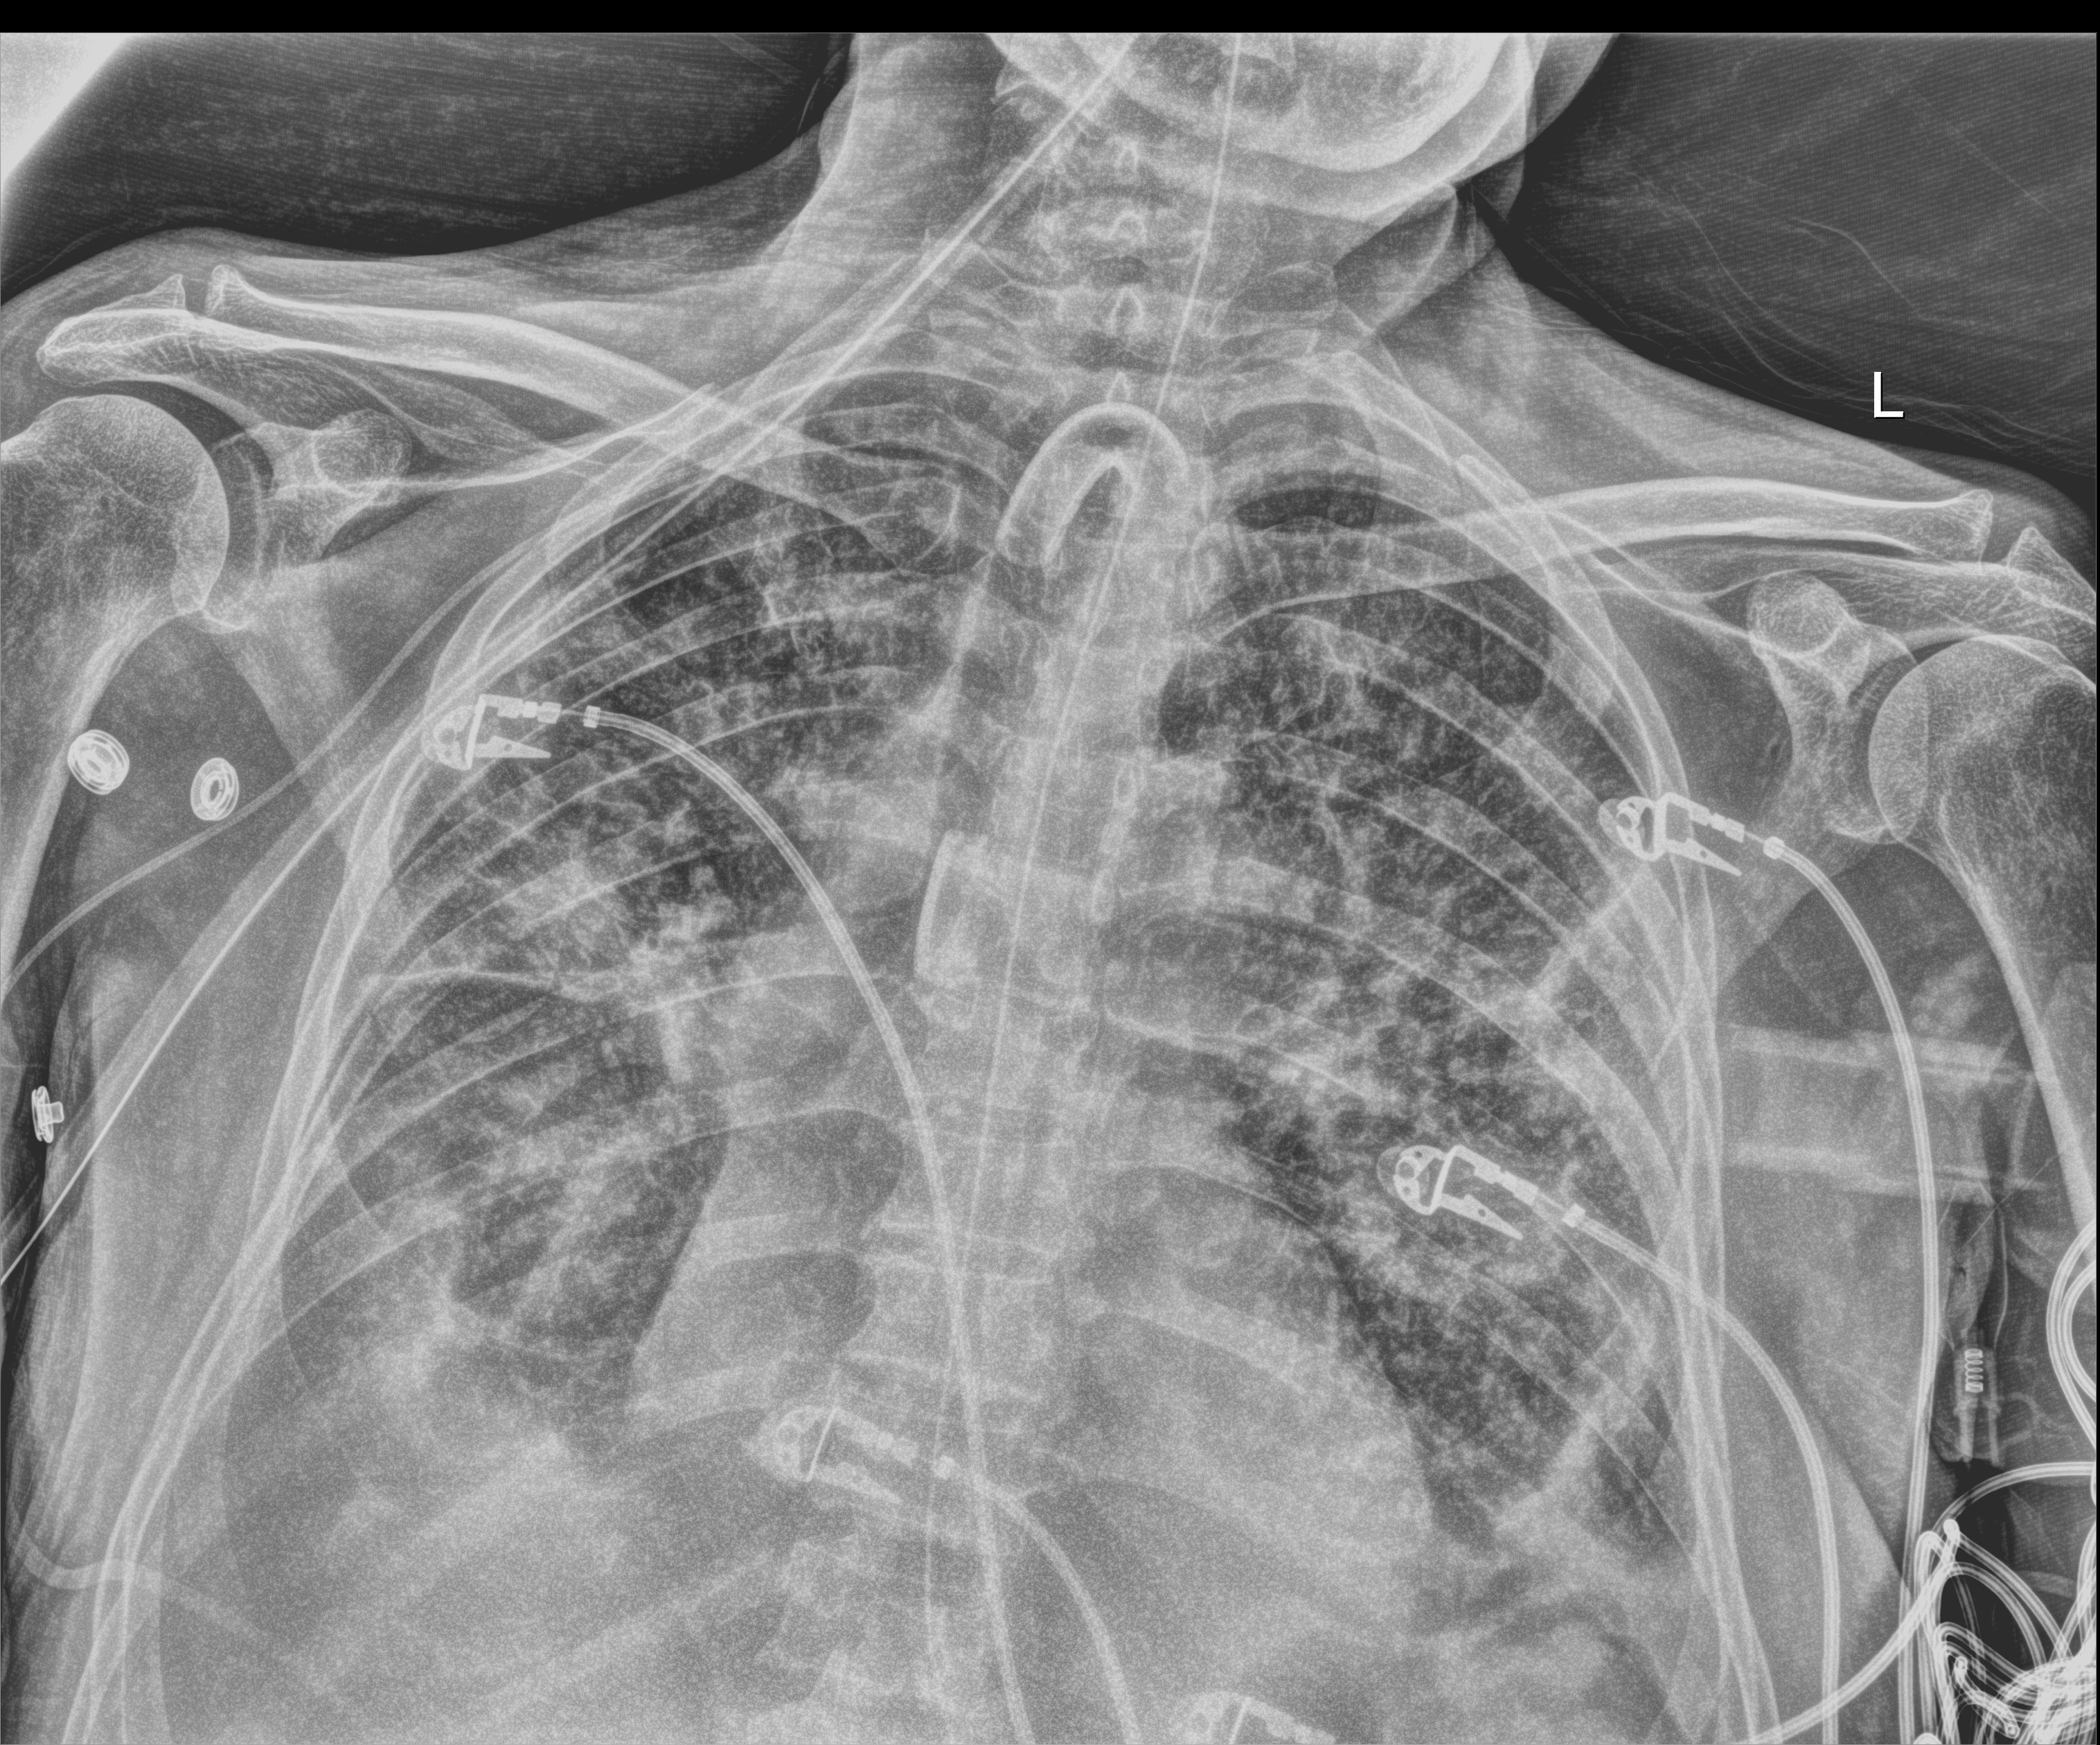
Chest X-ray (portable); anteroposterior (AP) projection. Patient hospitalised with COVID-19; male, aged 75–90 years.
Admission-level facts for this patient (not findings on this image; timing relative to this image not recorded): mechanically ventilated during this hospital stay: yes; admitted to intensive care during this hospital stay: yes.